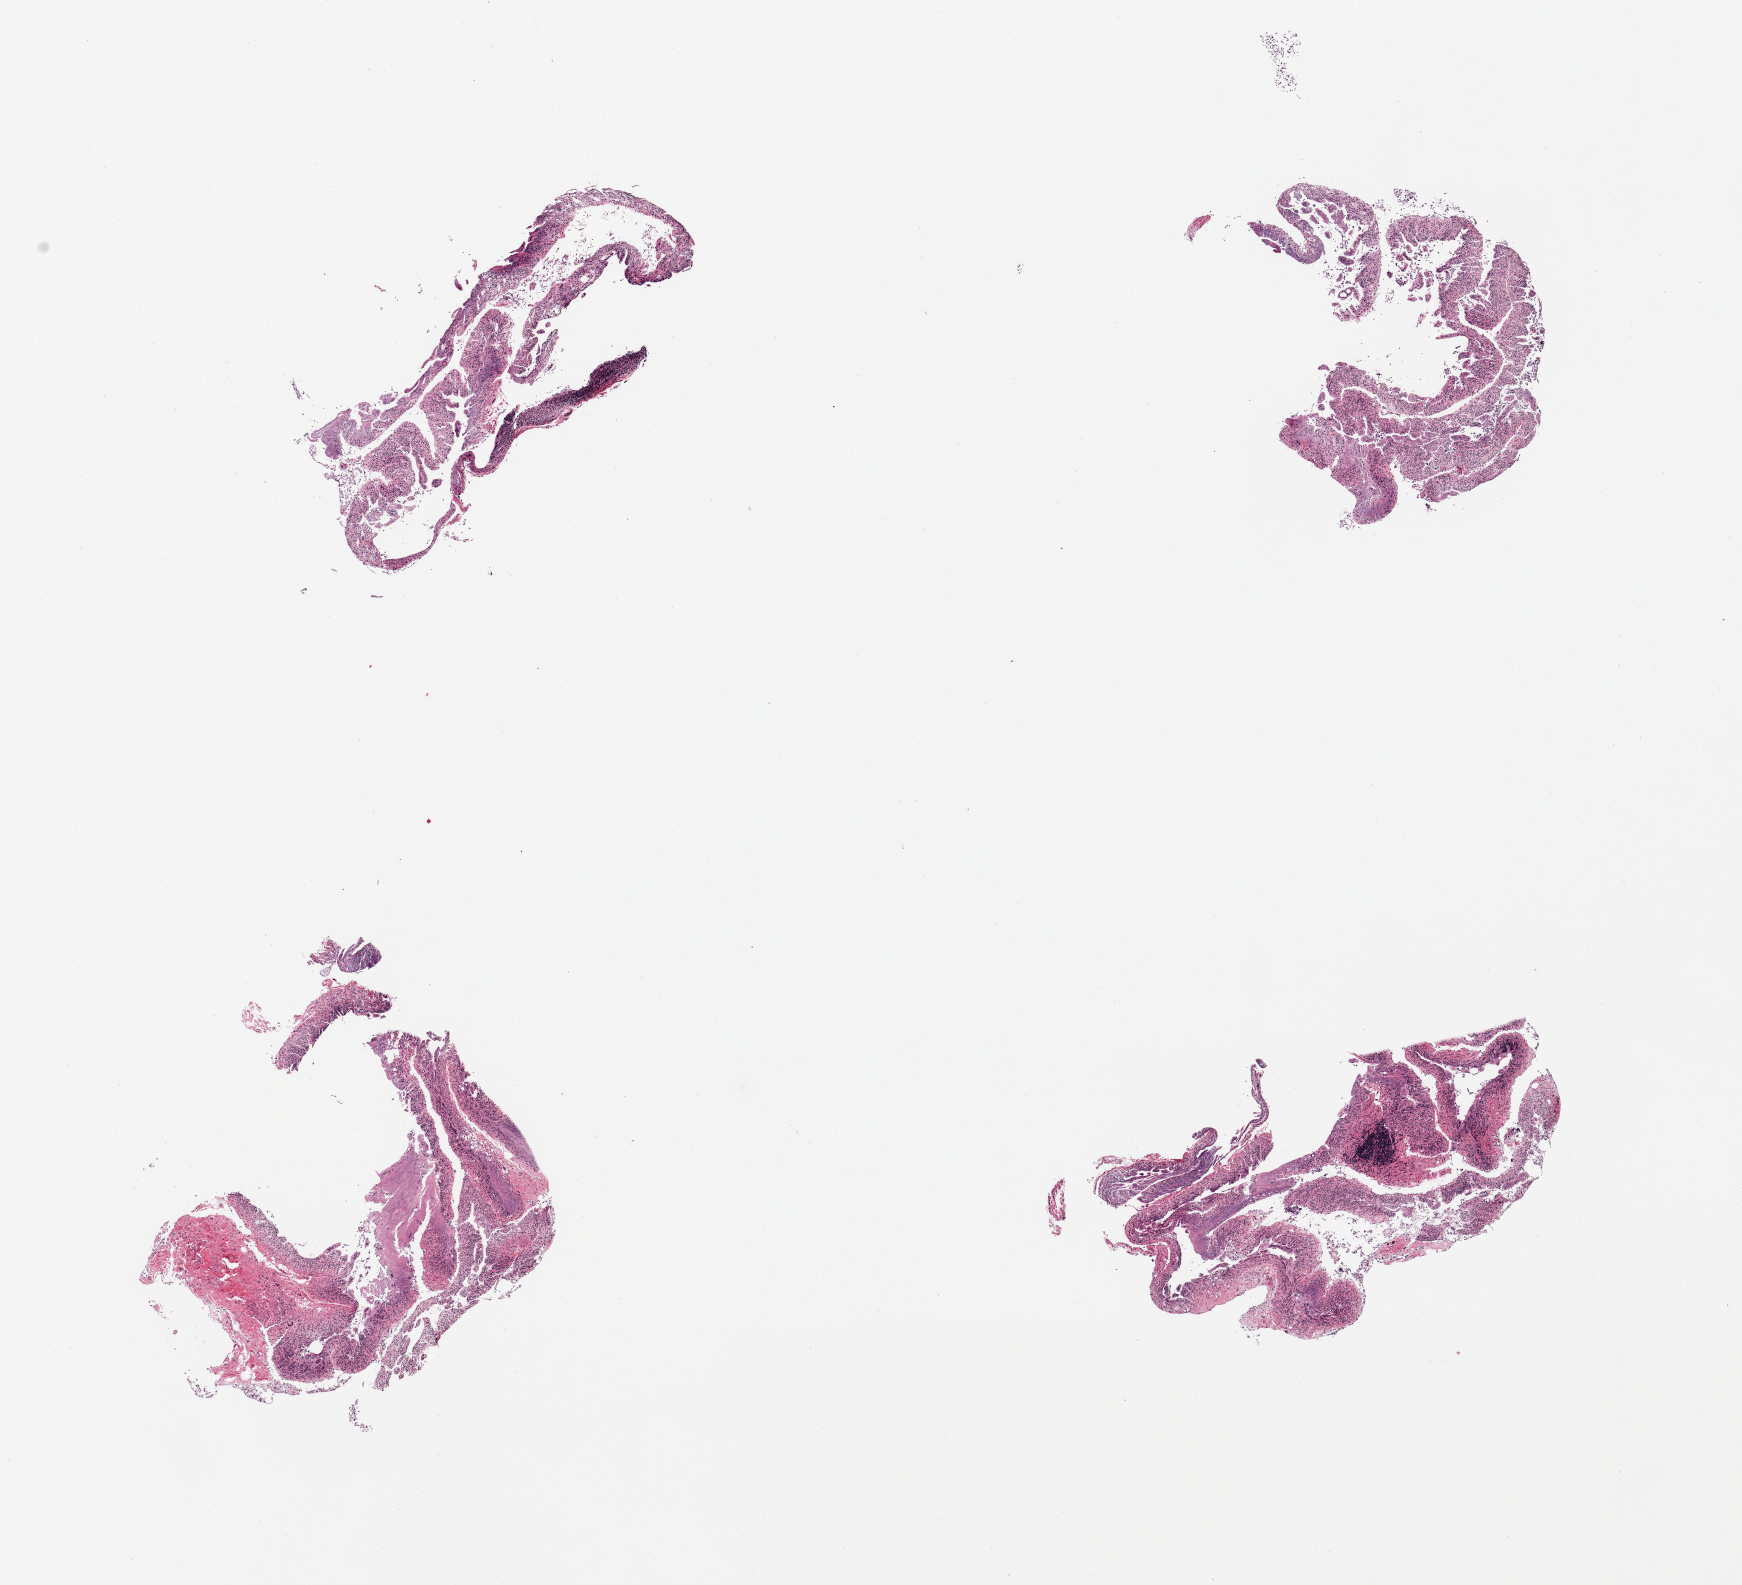
Digitized haematoxylin and eosin-stained section — shown as a low-resolution overview of the whole scanned area (about 13.8 x 12.5 mm). PAXgene-fixed, paraffin-embedded tissue. Section of ileum (target tissue). Tissue donor sample. Donor sex: male.
Pathologist's review note for this sample: 4 pieces; 1 very small lymphoid nodule; mucosa autolyzed.